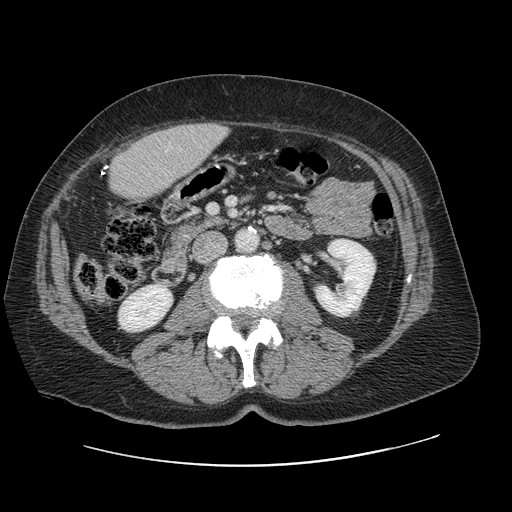
Contrast-enhanced abdominal CT, one axial slice. Slice 22 of 138 in the series (ordered by position). Soft-tissue window (W 400 / L 40 HU). 2.5 mm slice thickness. 512 × 512 image matrix. Male patient, age 71 years. From the clinical record (not read from this slice): diagnosis: colorectal cancer liver metastases, imaged before liver resection; multiple liver metastases: no; largest metastasis: 3.3 cm; disease in both lobes: no.
Annotated regions visible in this slice (manually delineated by an expert):
- liver: bounding box [x1, y1, x2, y2] px = [110, 124, 227, 201]
- planned liver remnant (the part of the liver to remain after resection): [109, 135, 177, 200]